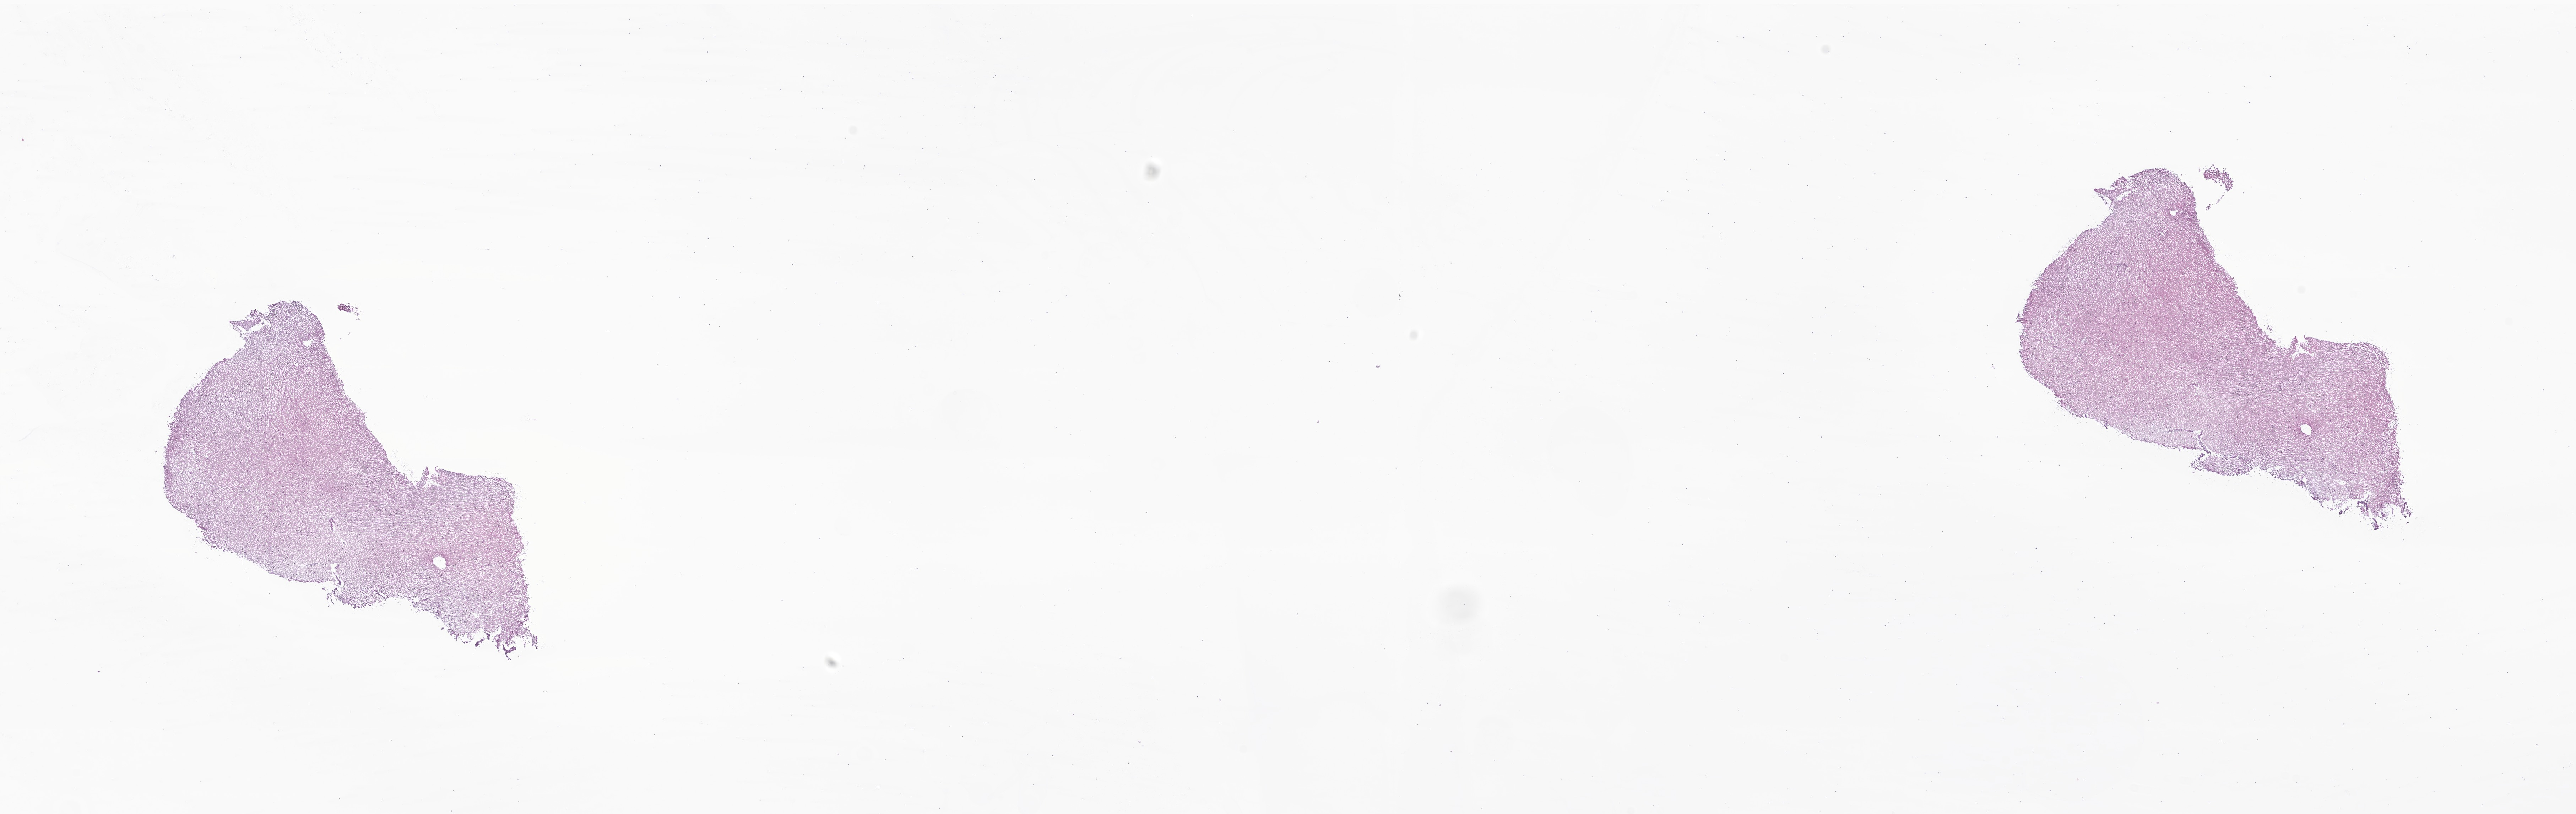
H&E whole-slide image of tumor tissue from the brain, a low-resolution overview of the entire scanned area, about 30.6 x 9.7 mm. Frozen section (OCT-embedded). Female patient, age 85 months (7 years 1 month).
• diagnosis: Pilocytic astrocytoma